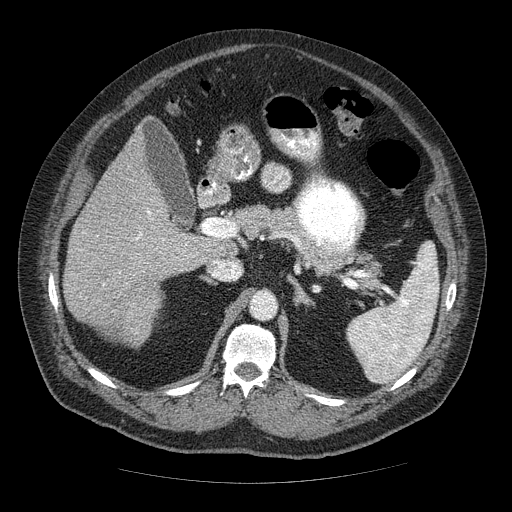
Contrast-enhanced abdominal CT (liver protocol), one axial slice. Slice 29 of 85 in the series (ordered by position). Reconstruction kernel STANDARD. Soft-tissue window (W 400 / L 40 HU). 2.5 mm slice thickness. 512 × 512 image matrix. From the clinical record (not read from this slice): diagnosis: hepatocellular carcinoma (patient treated with transarterial chemoembolisation; whether this scan precedes or follows treatment is not stated here); TNM stage (as recorded): Stage-IIIA; Child-Pugh class: A; tumour nodularity: multinodular; tumour size: 7 cm.
Outlined on this slice (semi-automatically segmented with operator editing):
- liver parenchyma outside the tumour (the mass and vessels are separate outlines, so this box may not span the whole liver): bounding box (x1, y1, x2, y2) in pixels: (64, 126, 226, 342)
- mass: (110, 282, 158, 344)
- liver vessels: (135, 210, 187, 245)